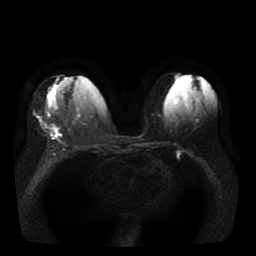
Breast MRI, one axial slice; position 16 of 41 along the scan axis; diffusion-weighted series; image 2 of 4 stored at this slice position (different b-values; order by instance number); 1.5 T; 5 mm slice thickness; 256 × 256 image matrix, field of view 330 × 330 mm. Female patient.
Structures marked on this image (outlined manually by an expert reader):
- tumour on diffusion-weighted imaging: bounding box <43,123,60,135> (left, top, right, bottom; pixels)